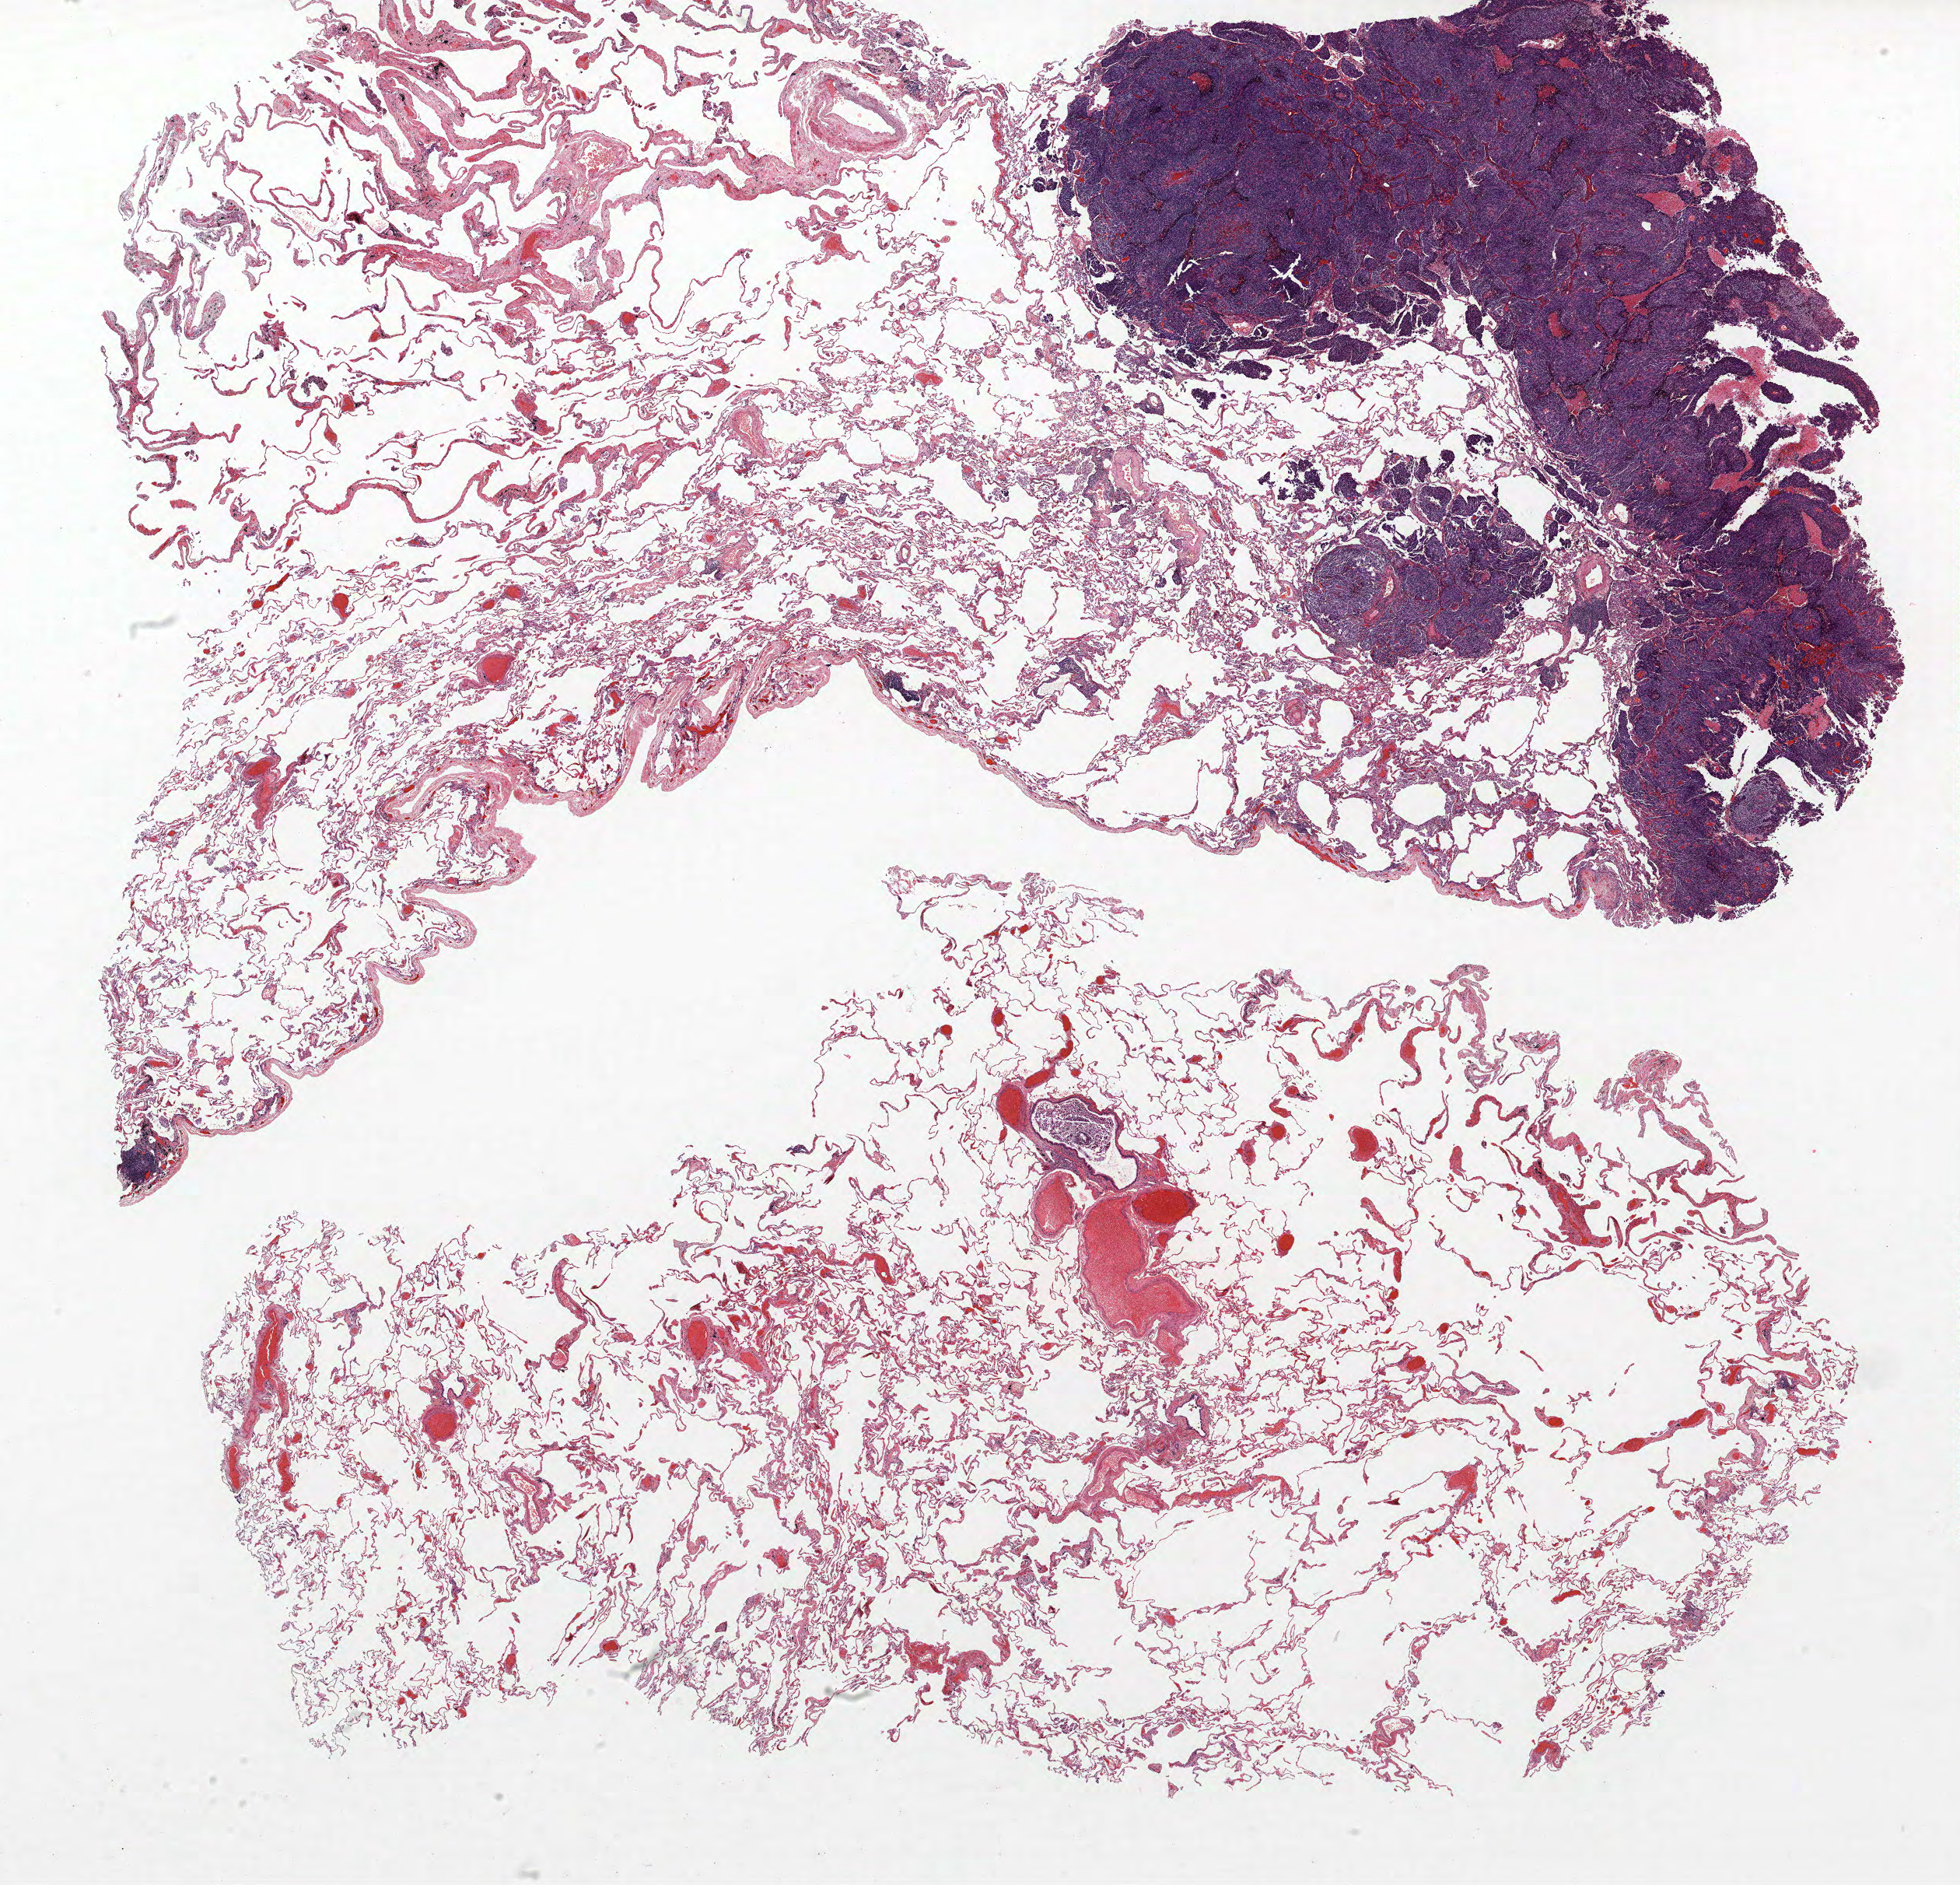
H&E whole-slide image, a low-resolution overview of the entire scanned area, about 20.2 x 19.4 mm (from a 40x scan); FFPE section; lung tissue. Female patient, aged 70 at enrolment. Former smoker at enrolment.
Stage (AJCC 6th edition): IA. ICD-O-3 topography: upper lobe of lung (C34.1). Primary tumour location (clinical record): right upper lobe. Tumour size (pathology): 30 mm. Participant's lung-cancer diagnosis: Large cell neuroendocrine carcinoma.